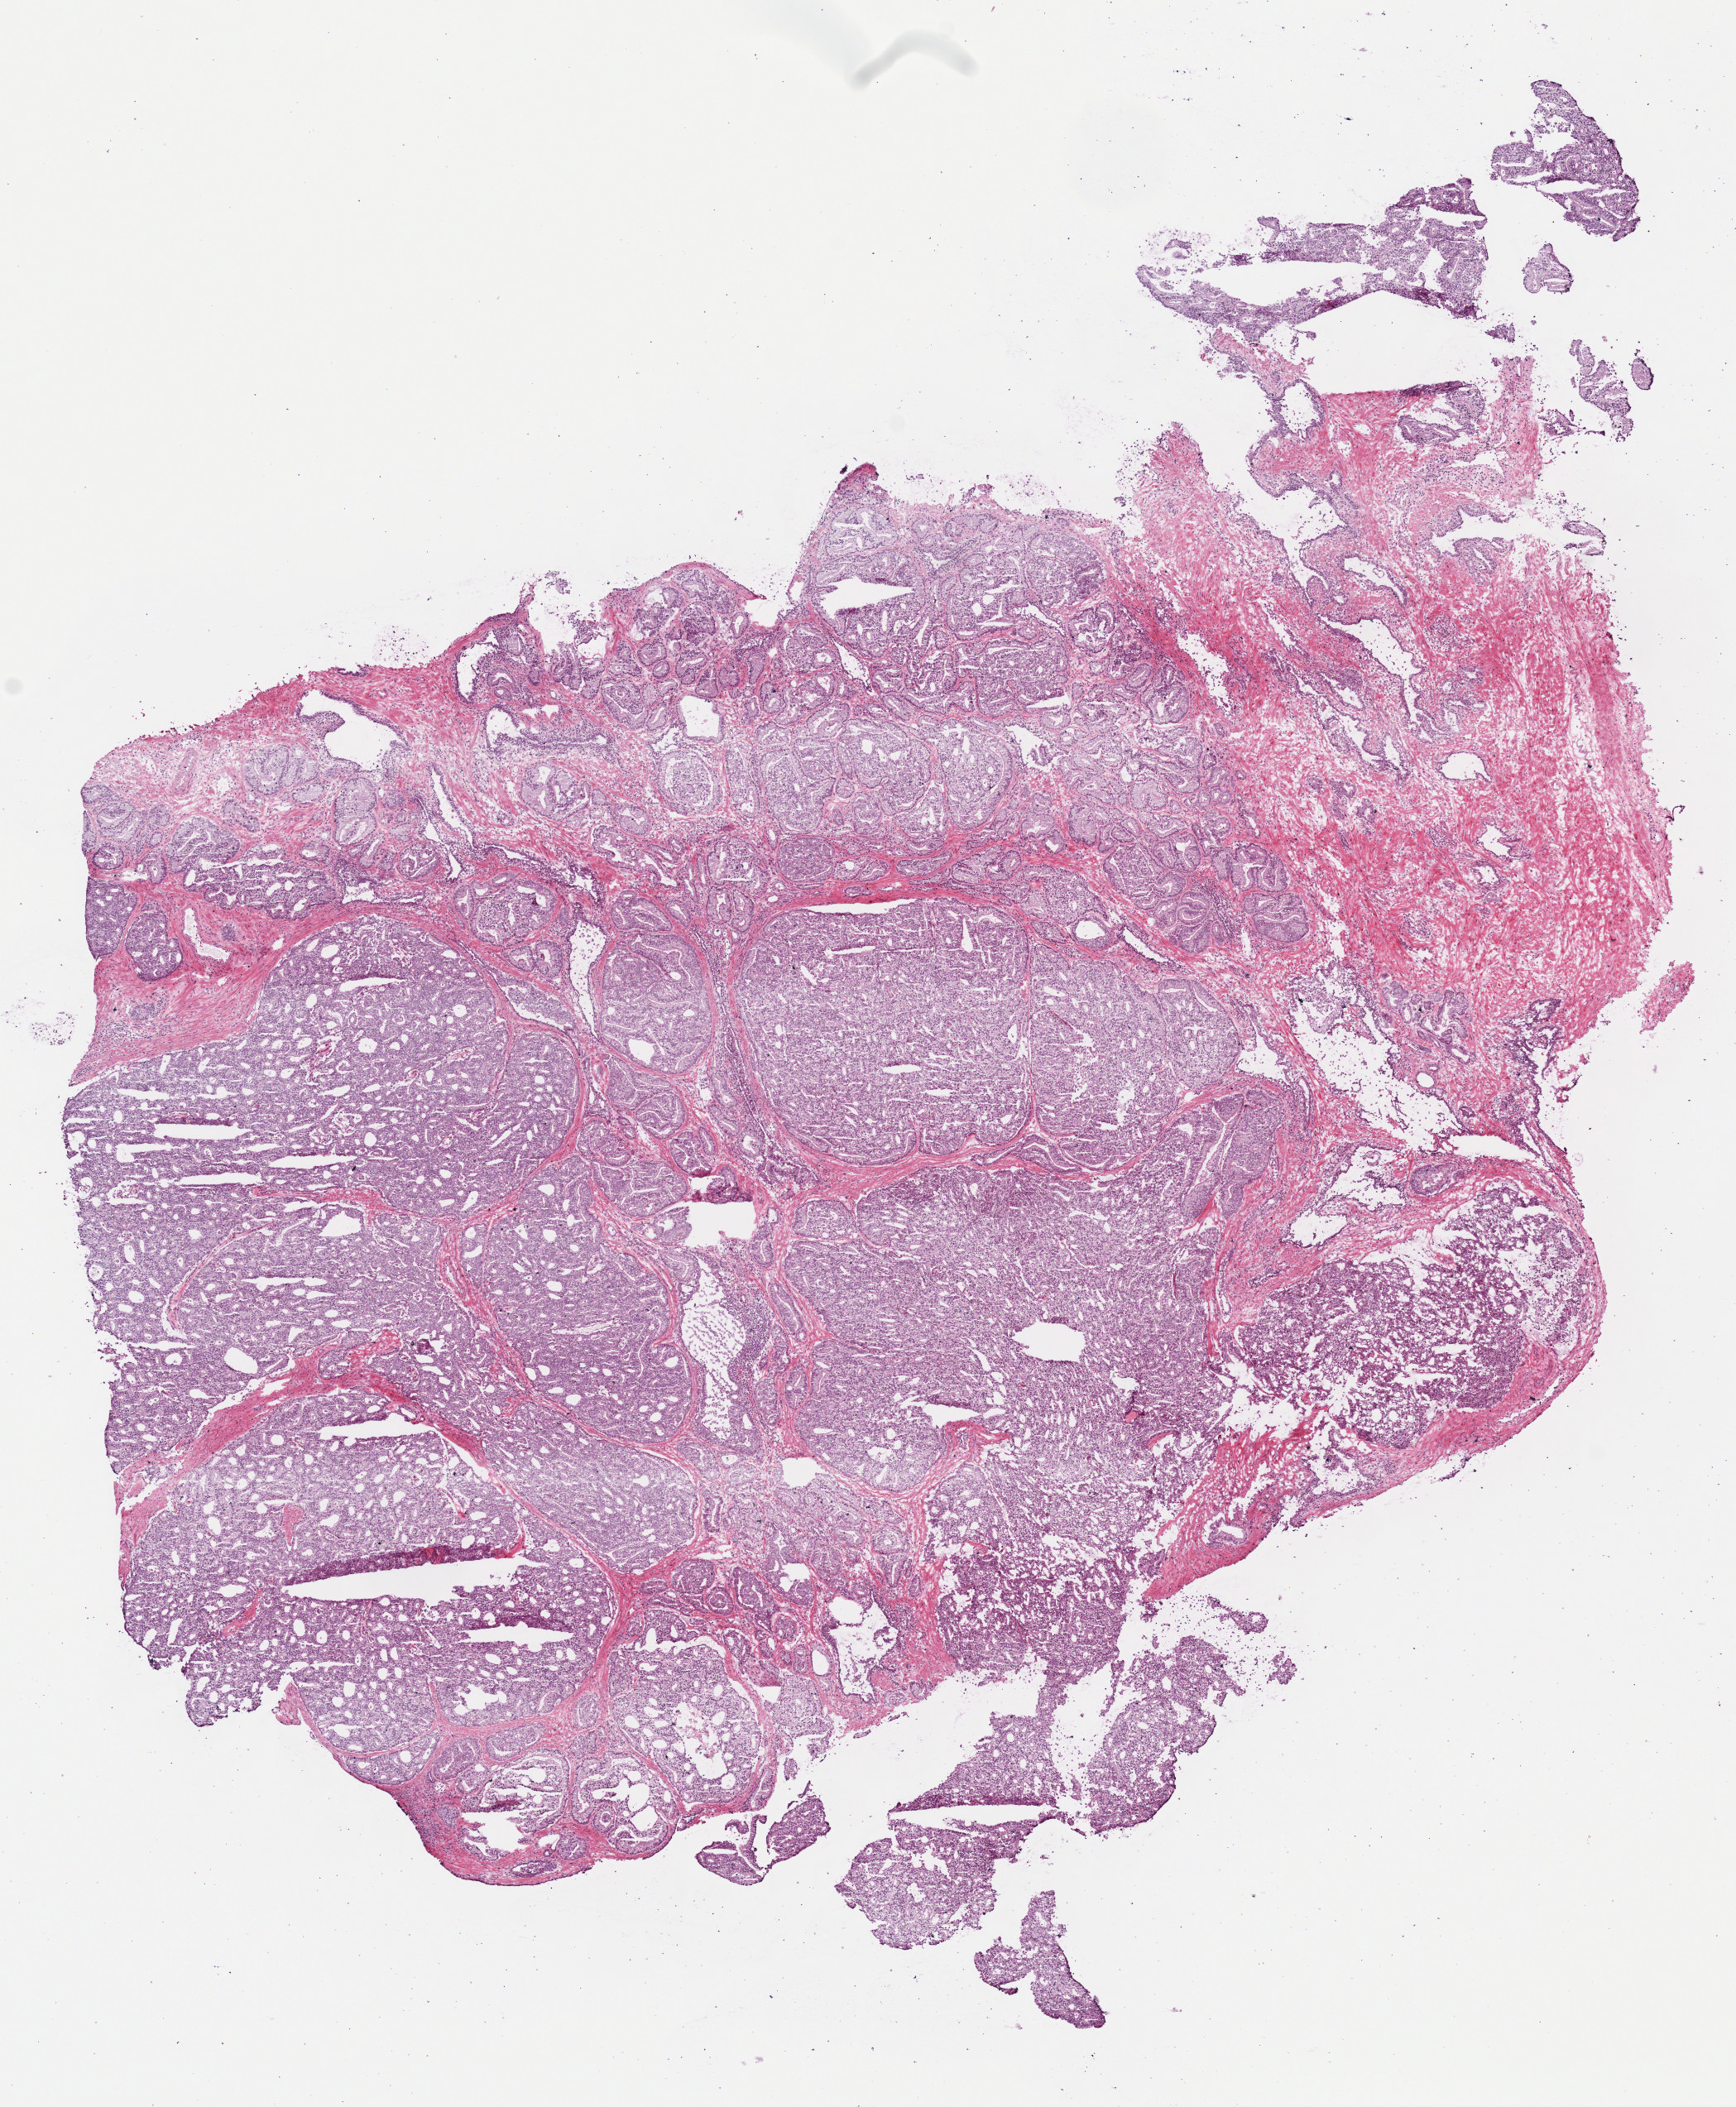
H&E whole-slide image, whole scanned area (about 8.5 x 10.3 mm, acquisition: 40x scan) shown as a low-resolution overview. Frozen section. Primary tumour sample from the prostate. Male, age 52 years at initial diagnosis. Pathologist review of this section (percent, as recorded): tumour cells 85%, tumour nuclei 90%.
Diagnosis: Adenocarcinoma, NOS (prostate gland).